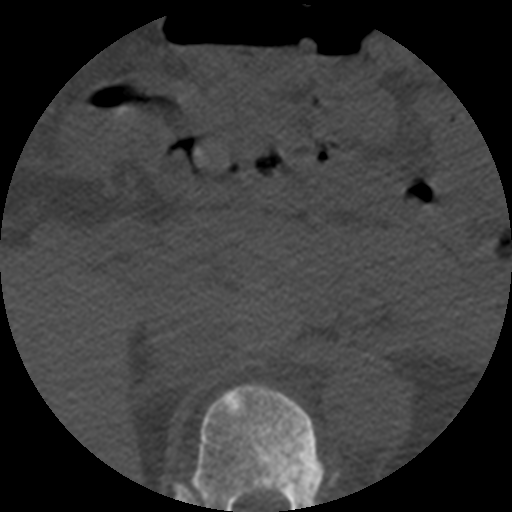
CT including the spine, one axial slice. Position 244 of 508 along the scan axis. 120 kVp. Bone window (W 1800 / L 400 HU). 512 × 512 image matrix. Patient age 57 years. From the clinical record (not read from this slice): primary cancer: prostate.
Outlined on this slice (semi-automatically segmented with operator editing):
- T11 vertebra: bounding box <193,384,324,512> (left, top, right, bottom; pixels)